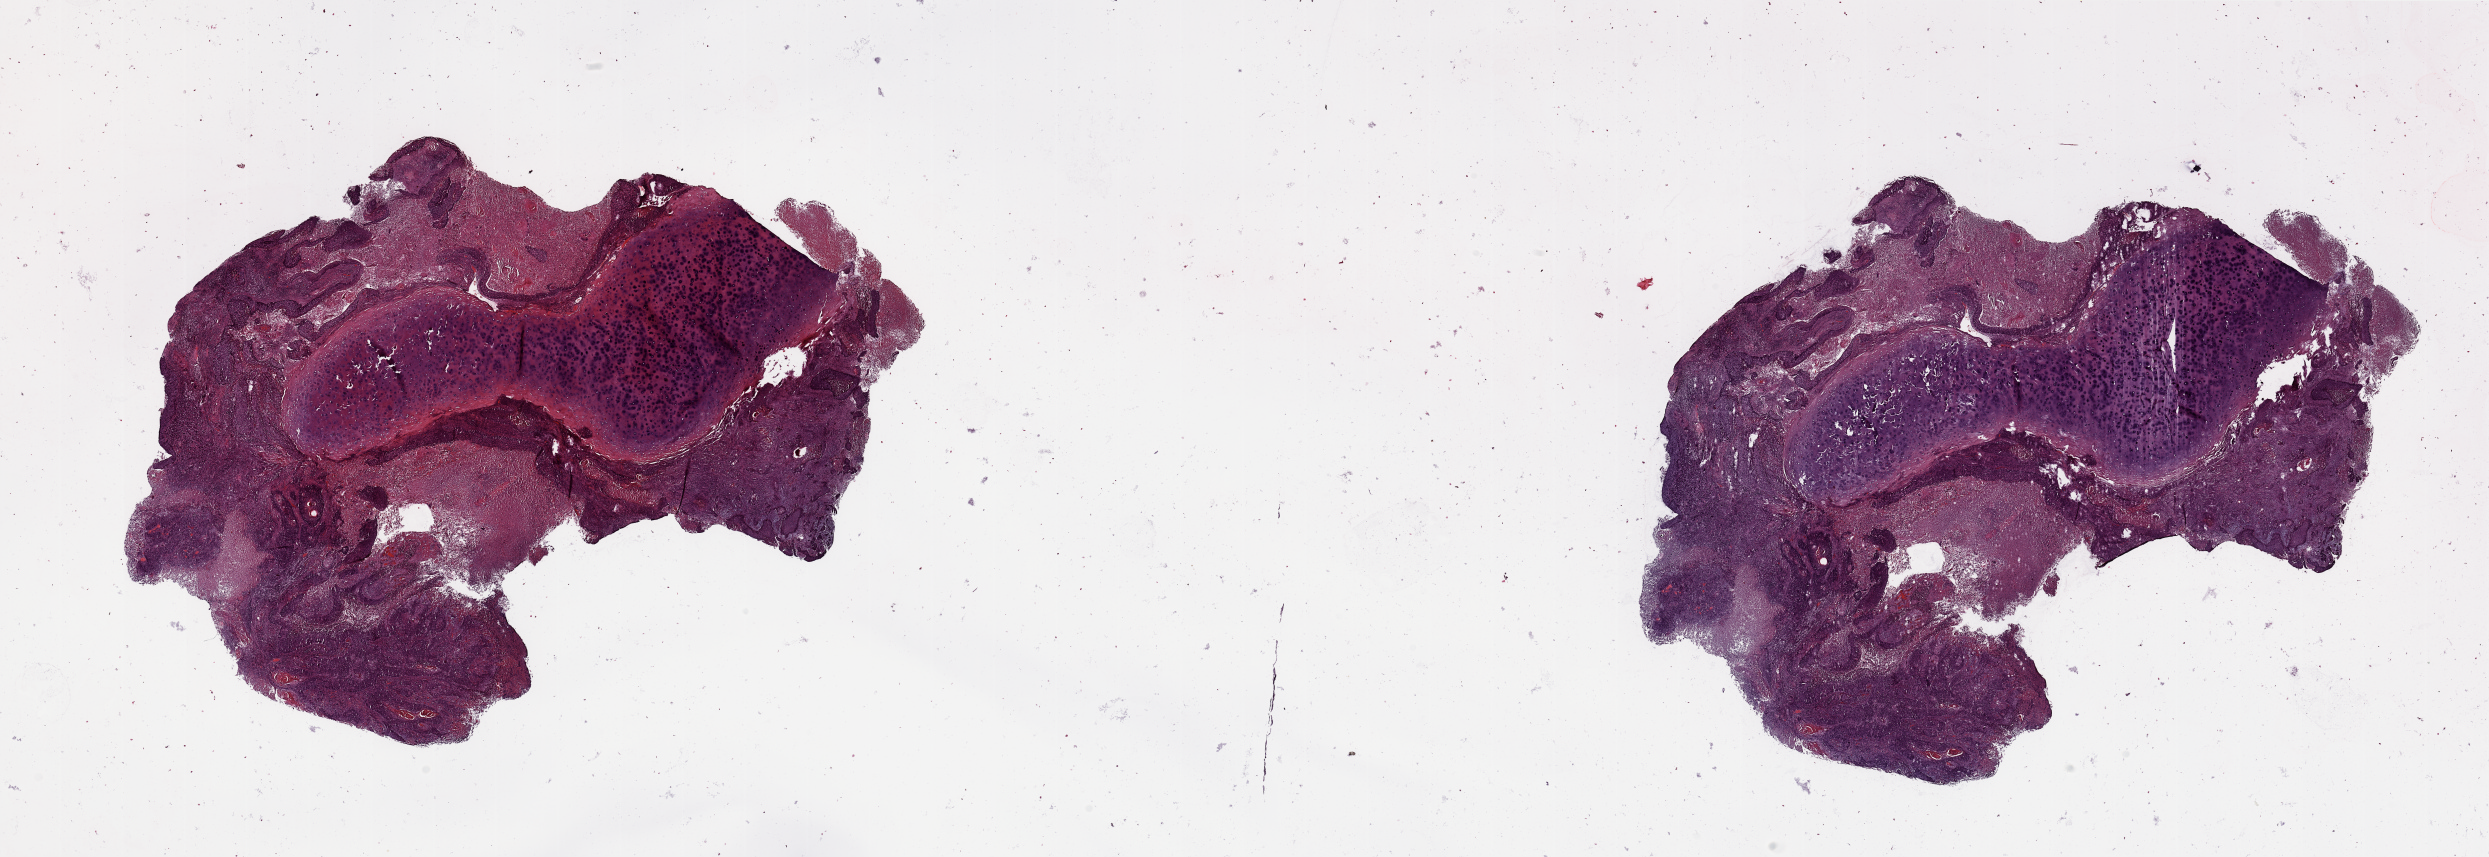
Whole-slide histology image, Hematoxylin and eosin (H&E) stained — whole scanned area (about 39.4 x 13.6 mm, from a 20x scan) shown as a low-resolution overview. Lung, tumour tissue. Male, 66 y/o. Histologic grade: G2 (moderately differentiated).
AJCC pathologic stage: IIA. Diagnosis: Squamous cell carcinoma, NOS. Primary tumour site (as recorded): left upper lobe.